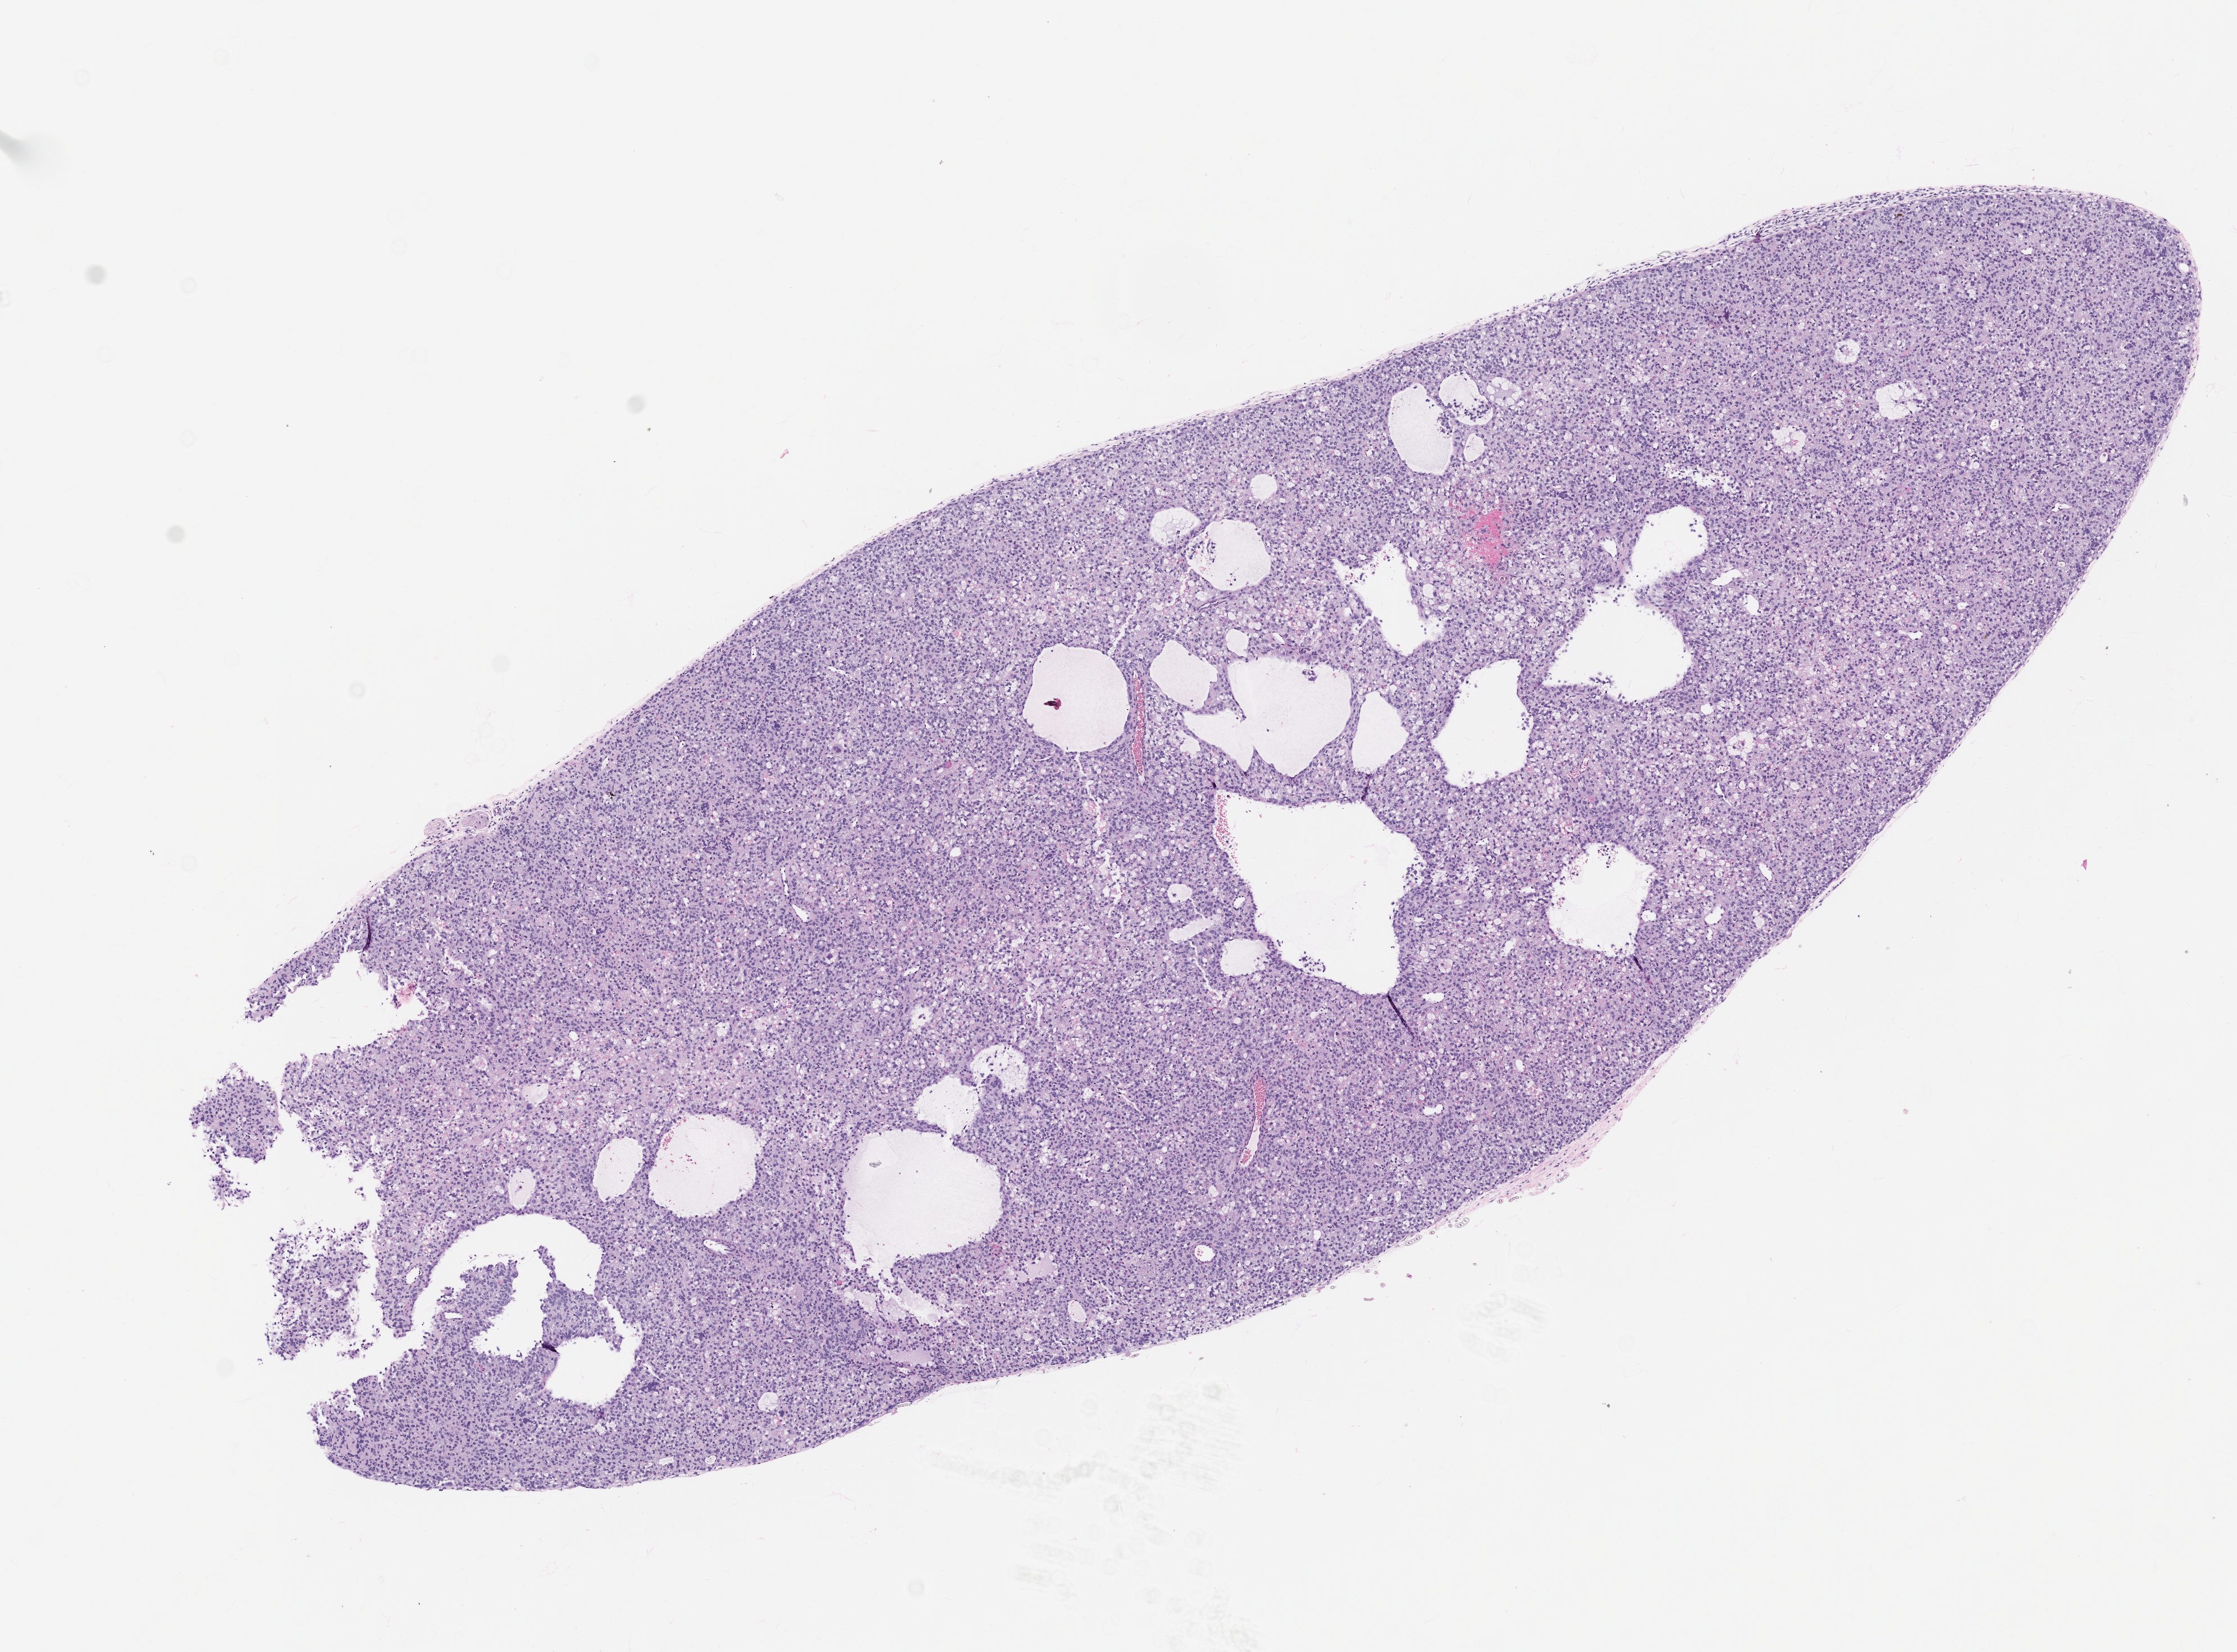
H&E whole-slide image of a patient-derived xenograft (PDX) tumor grown in a mouse, passage 2, low-resolution overview of the scanned area, about 8.0 x 5.9 mm. Formalin-fixed paraffin-embedded section. Originating tumor site category: uterus.
Originating patient diagnosis: Leiomyosarcoma.